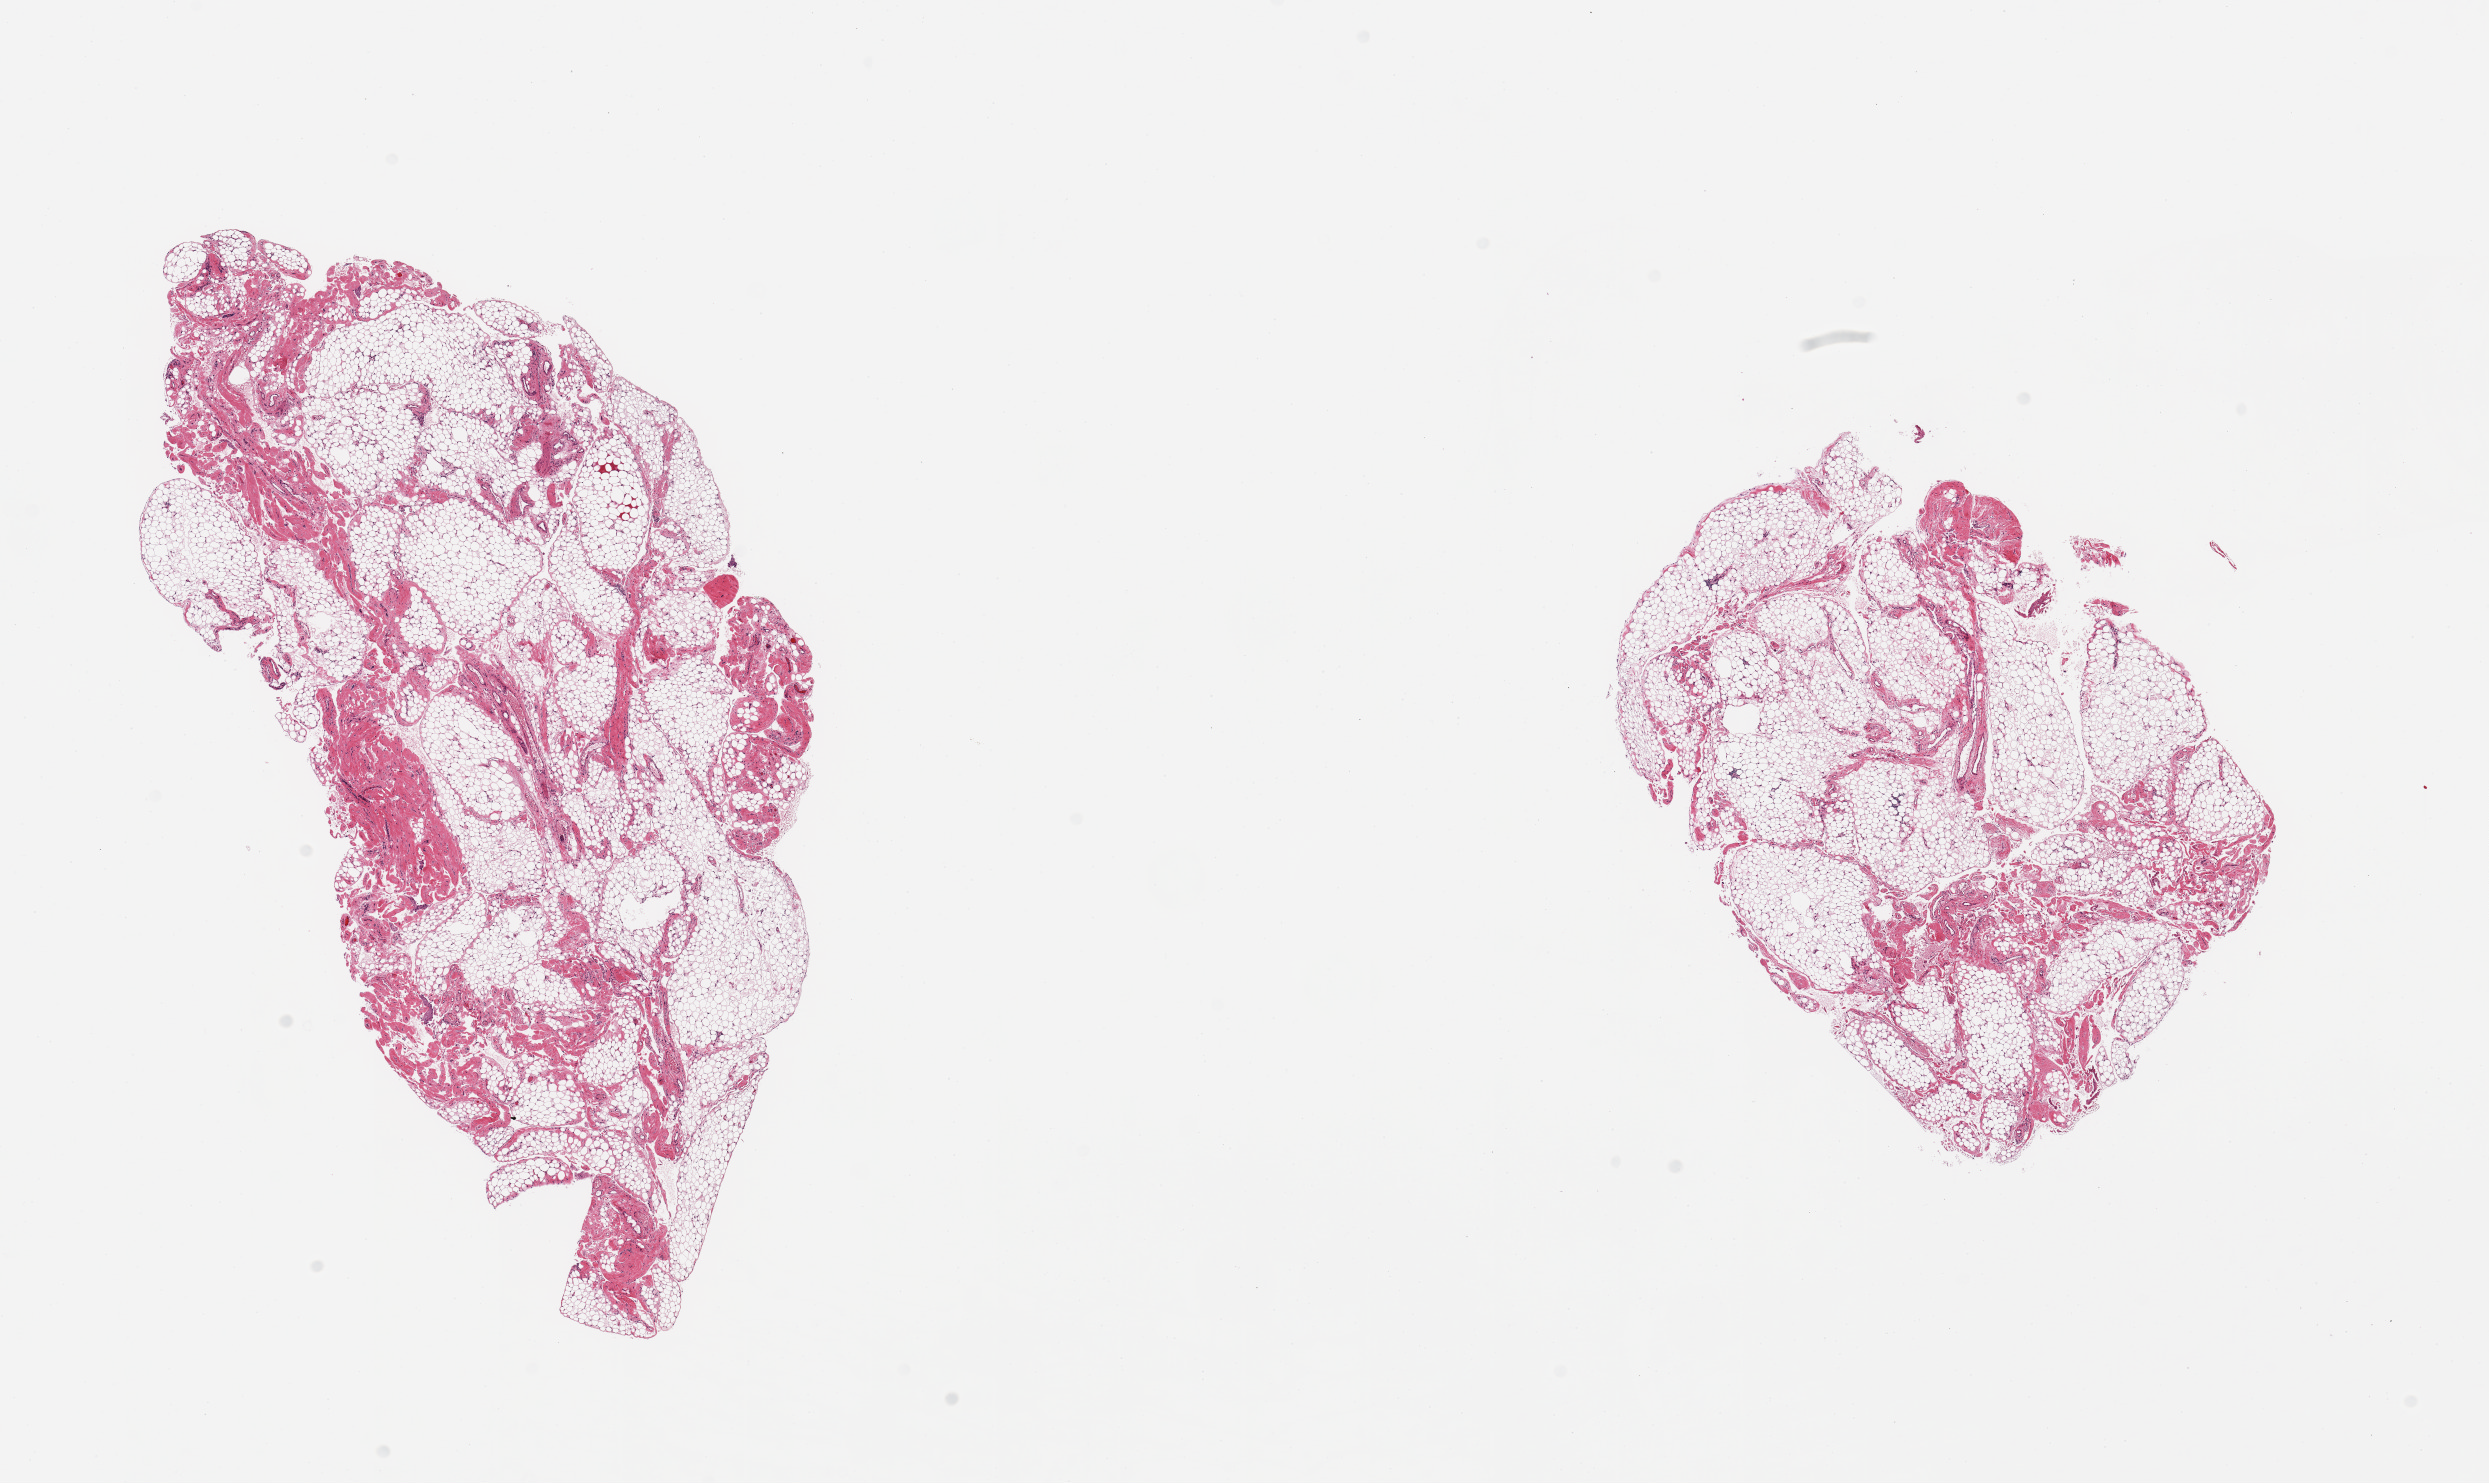
Digitized hematoxylin and eosin (H&E)-stained section — whole scanned area (about 19.7 x 11.7 mm, acquisition: 20x scan) shown as a low-resolution overview. PAXgene-fixed paraffin-embedded (PFPE) section. Section of omentum (target tissue). Tissue donor sample. Donor: male.
- reviewer comment on this tissue sample: 2 pieces; 10% fibrofatty content